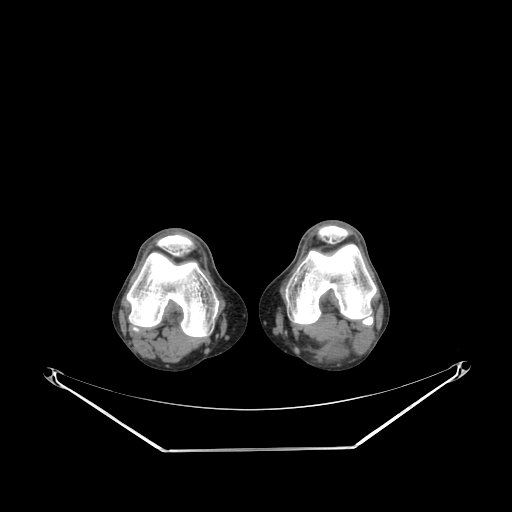
CT of an extremity soft-tissue mass (from a PET/CT study), one axial slice; reconstruction kernel SOFT; soft-tissue window (W 400 / L 40 HU); 3.75 mm slice thickness; 512 × 512 image matrix, field of view 500 × 500 mm. Male patient. Case-level facts recorded for this patient, not image findings: histological type: synovial sarcoma; site of the primary tumour: left poplietal fossa.
Annotated regions visible in this slice (expert contour drawn on MRI and transferred to this co-registered scan by the dataset authors):
- gross tumour volume (mass): bounding box [x1, y1, x2, y2] px = [331, 340, 348, 360]